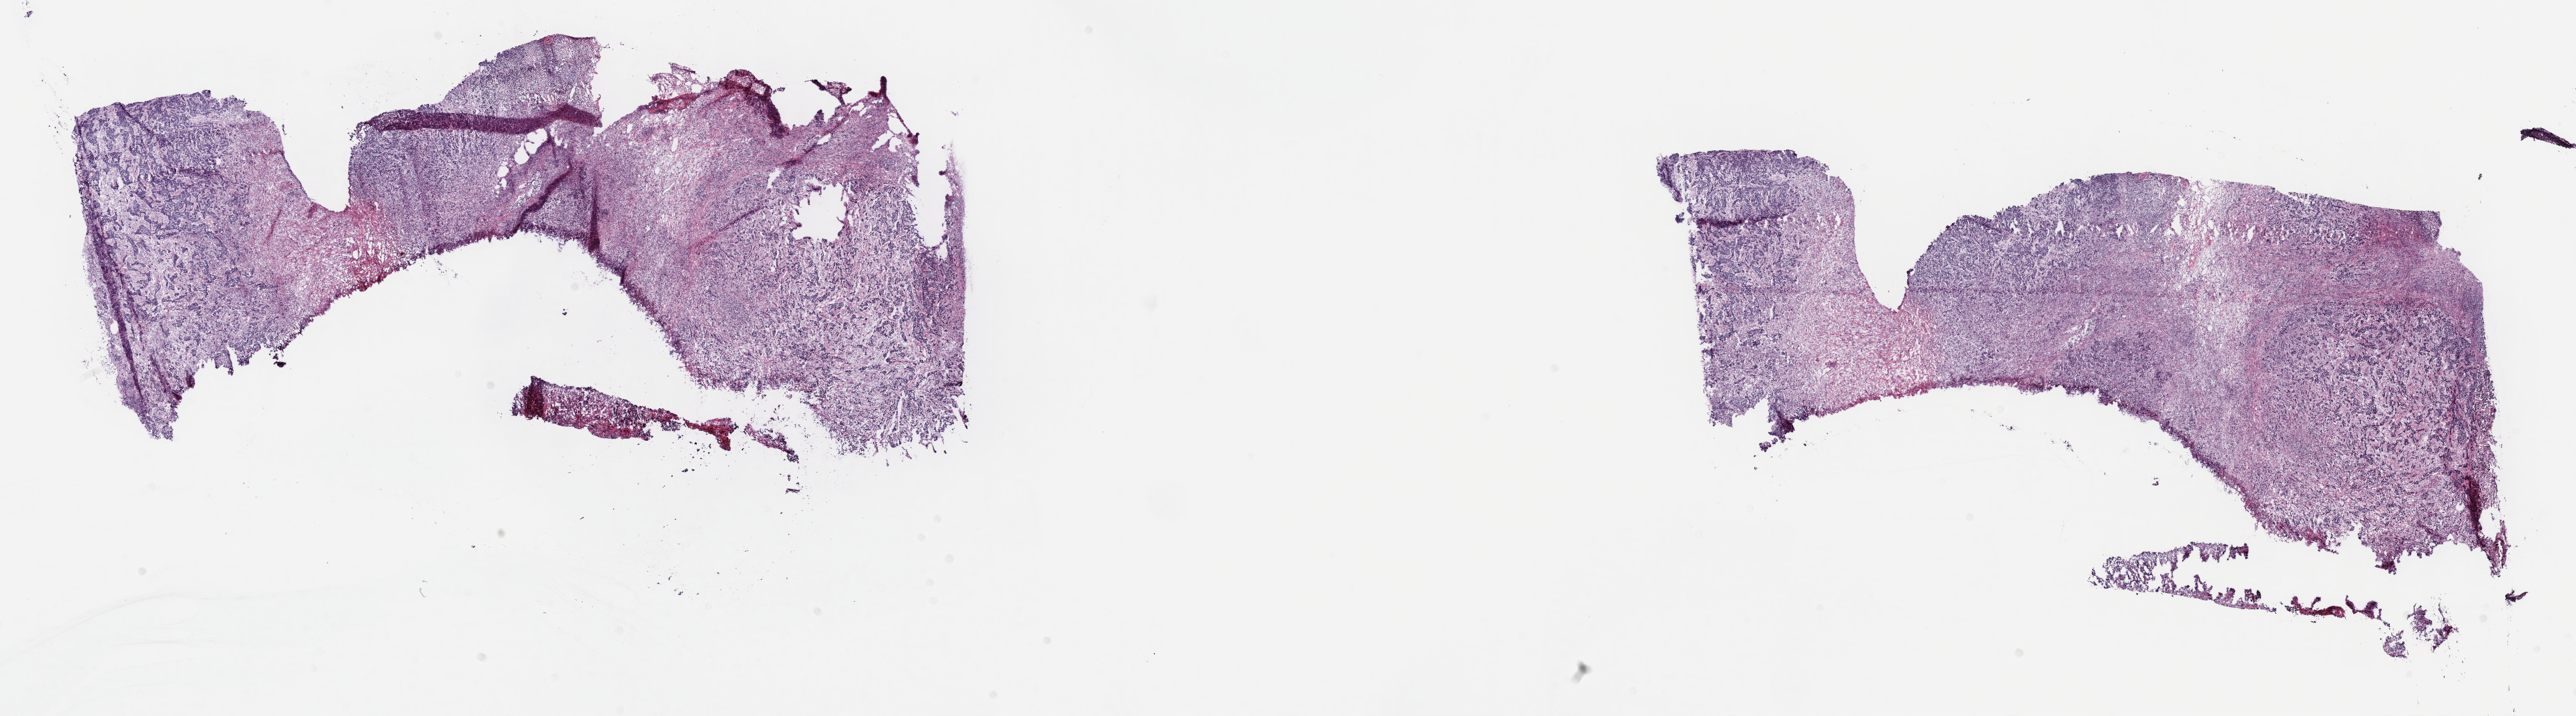
Digitized H&E tissue section (whole slide) — low-resolution overview of the scanned area, about 31.2 x 8.7 mm (from a 40x scan); frozen section from the top of the tissue portion; metastatic tumour sample, sampled site not recorded. Male, age 53 years at initial diagnosis. Slide review estimates, as recorded: tumour cells 100%, tumour nuclei 70%.
This section: metastatic tumour tissue. Patient diagnosis: Transitional cell carcinoma.